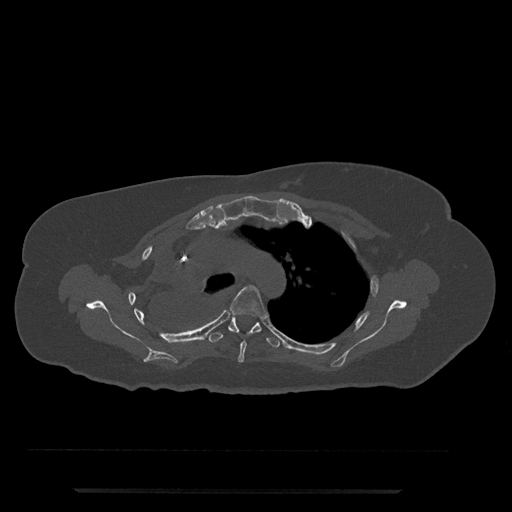
CT including the spine, one axial slice. Position 568 of 797 along the scan axis. Reconstruction kernel Br40s/3. 120 kVp. Bone window (W 1800 / L 400 HU). 512 × 512 image matrix, field of view 440 × 440 mm. Patient: female, 51 years. From the clinical record (not read from this slice): primary cancer: neuro.
Outlined on this slice (semi-automatically segmented with operator editing):
- T4 vertebra: bounding box <229,285,268,363> (left, top, right, bottom; pixels)
- T5 vertebra: <207,317,282,348>